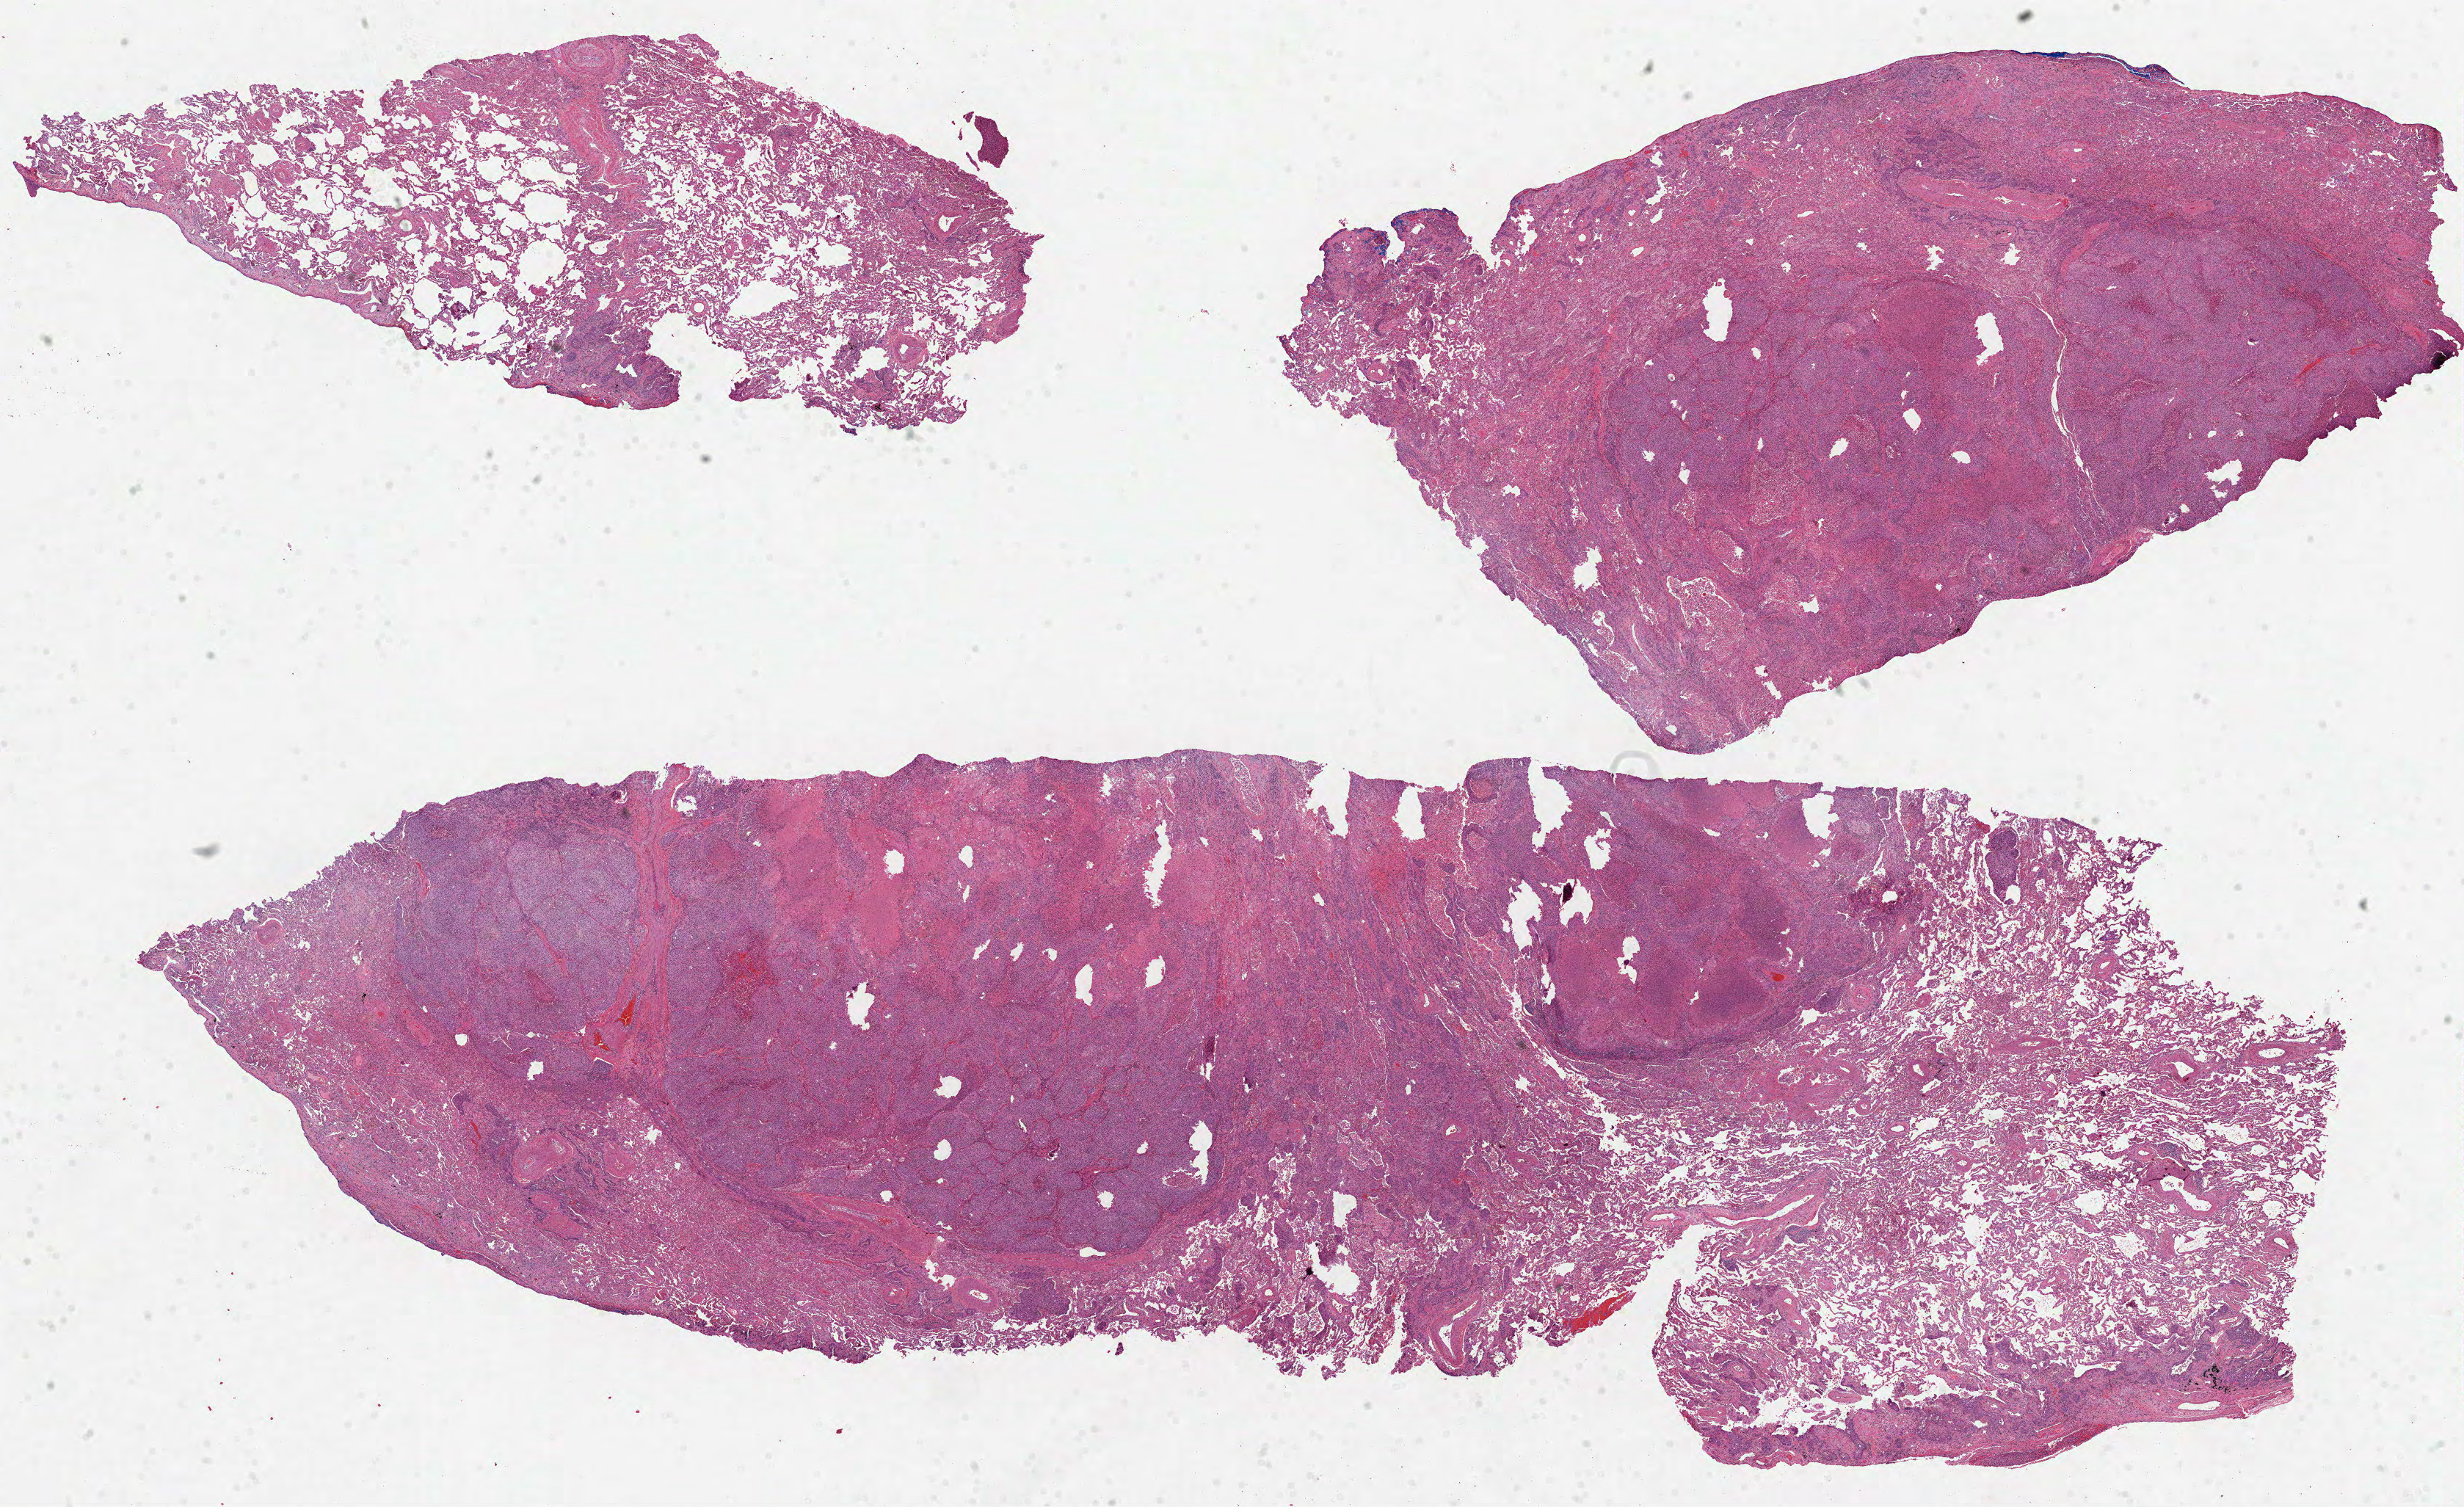
Whole-slide histology image, Hematoxylin and eosin (H&E) stained — shown as a low-resolution overview of the whole scanned area (about 27.1 x 16.6 mm, acquisition: 40x scan). Formalin-fixed paraffin-embedded (FFPE) diagnostic section. Sample: primary tumour, lung. Patient: male, age at initial diagnosis 79 years.
AJCC pathologic stage: IB. Pathologic diagnosis: Squamous cell carcinoma, NOS (lower lobe, lung). Laterality: right.